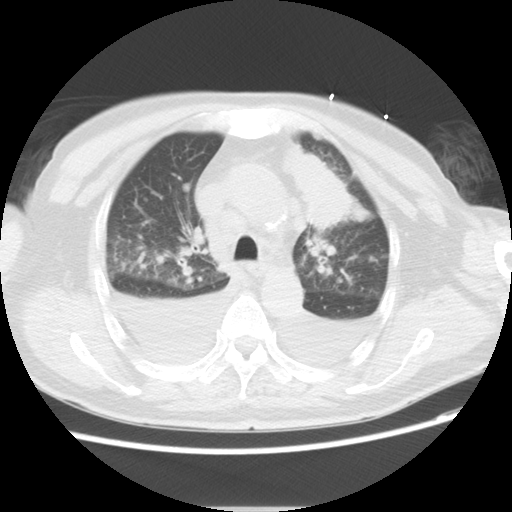
Chest CT, one axial slice. Slice 18 of 21 in the series (ordered by position). Reconstruction kernel STANDARD. Lung window (W 1500 / L -600 HU). 5 mm slice thickness. 512 × 512 image matrix. Male patient, age 66 years. From the clinical record (not read from this slice): clinical TNM (as recorded): T1c N0 M0.
Annotated regions visible in this slice (bounding box drawn by a radiologist):
- lung tumour (recorded histology: adenocarcinoma): bounding box <281,137,355,231> (left, top, right, bottom; pixels)